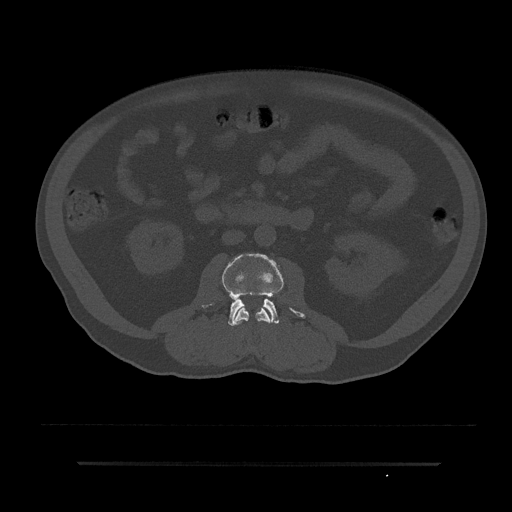
CT including the spine, one axial slice. Position 31 of 797 along the scan axis. 120 kVp. Bone window (W 1800 / L 400 HU). 0.5 mm slice thickness. 512 × 512 image matrix, field of view 464 × 464 mm. Patient: male, 59 years. From the clinical record (not read from this slice): primary cancer: bile ducts; vertebrae with lytic lesions (as recorded): T10.
Annotated regions visible in this slice (semi-automatically segmented with operator editing):
- L2 vertebra: box from (x=233, y=305) to (x=272, y=325) px
- L3 vertebra: (x=204, y=254)–(x=305, y=326)